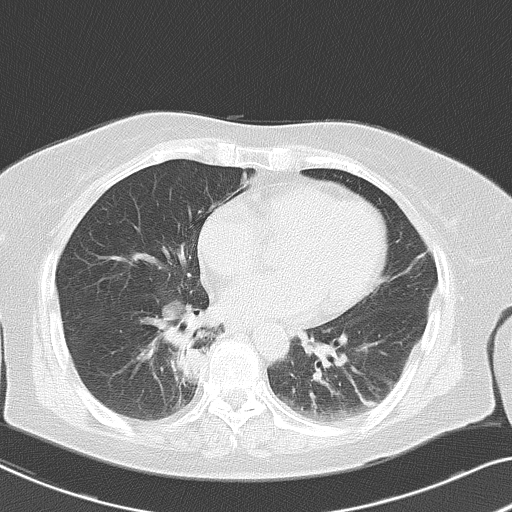
Chest CT, one axial slice; position 21 of 53 along the scan axis; 120 kVp; lung window (W 1500 / L -600 HU); 5 mm slice thickness; 512 × 512 image matrix. Patient: female, 70 years. Case-level facts recorded for this patient, not image findings: clinical TNM (as recorded): T2 N1 M1a.
Outlined on this slice (rectangle marked by the reading radiologist):
- lung tumour (recorded histology: adenocarcinoma): bounding box [x1, y1, x2, y2] px = [169, 328, 213, 389]